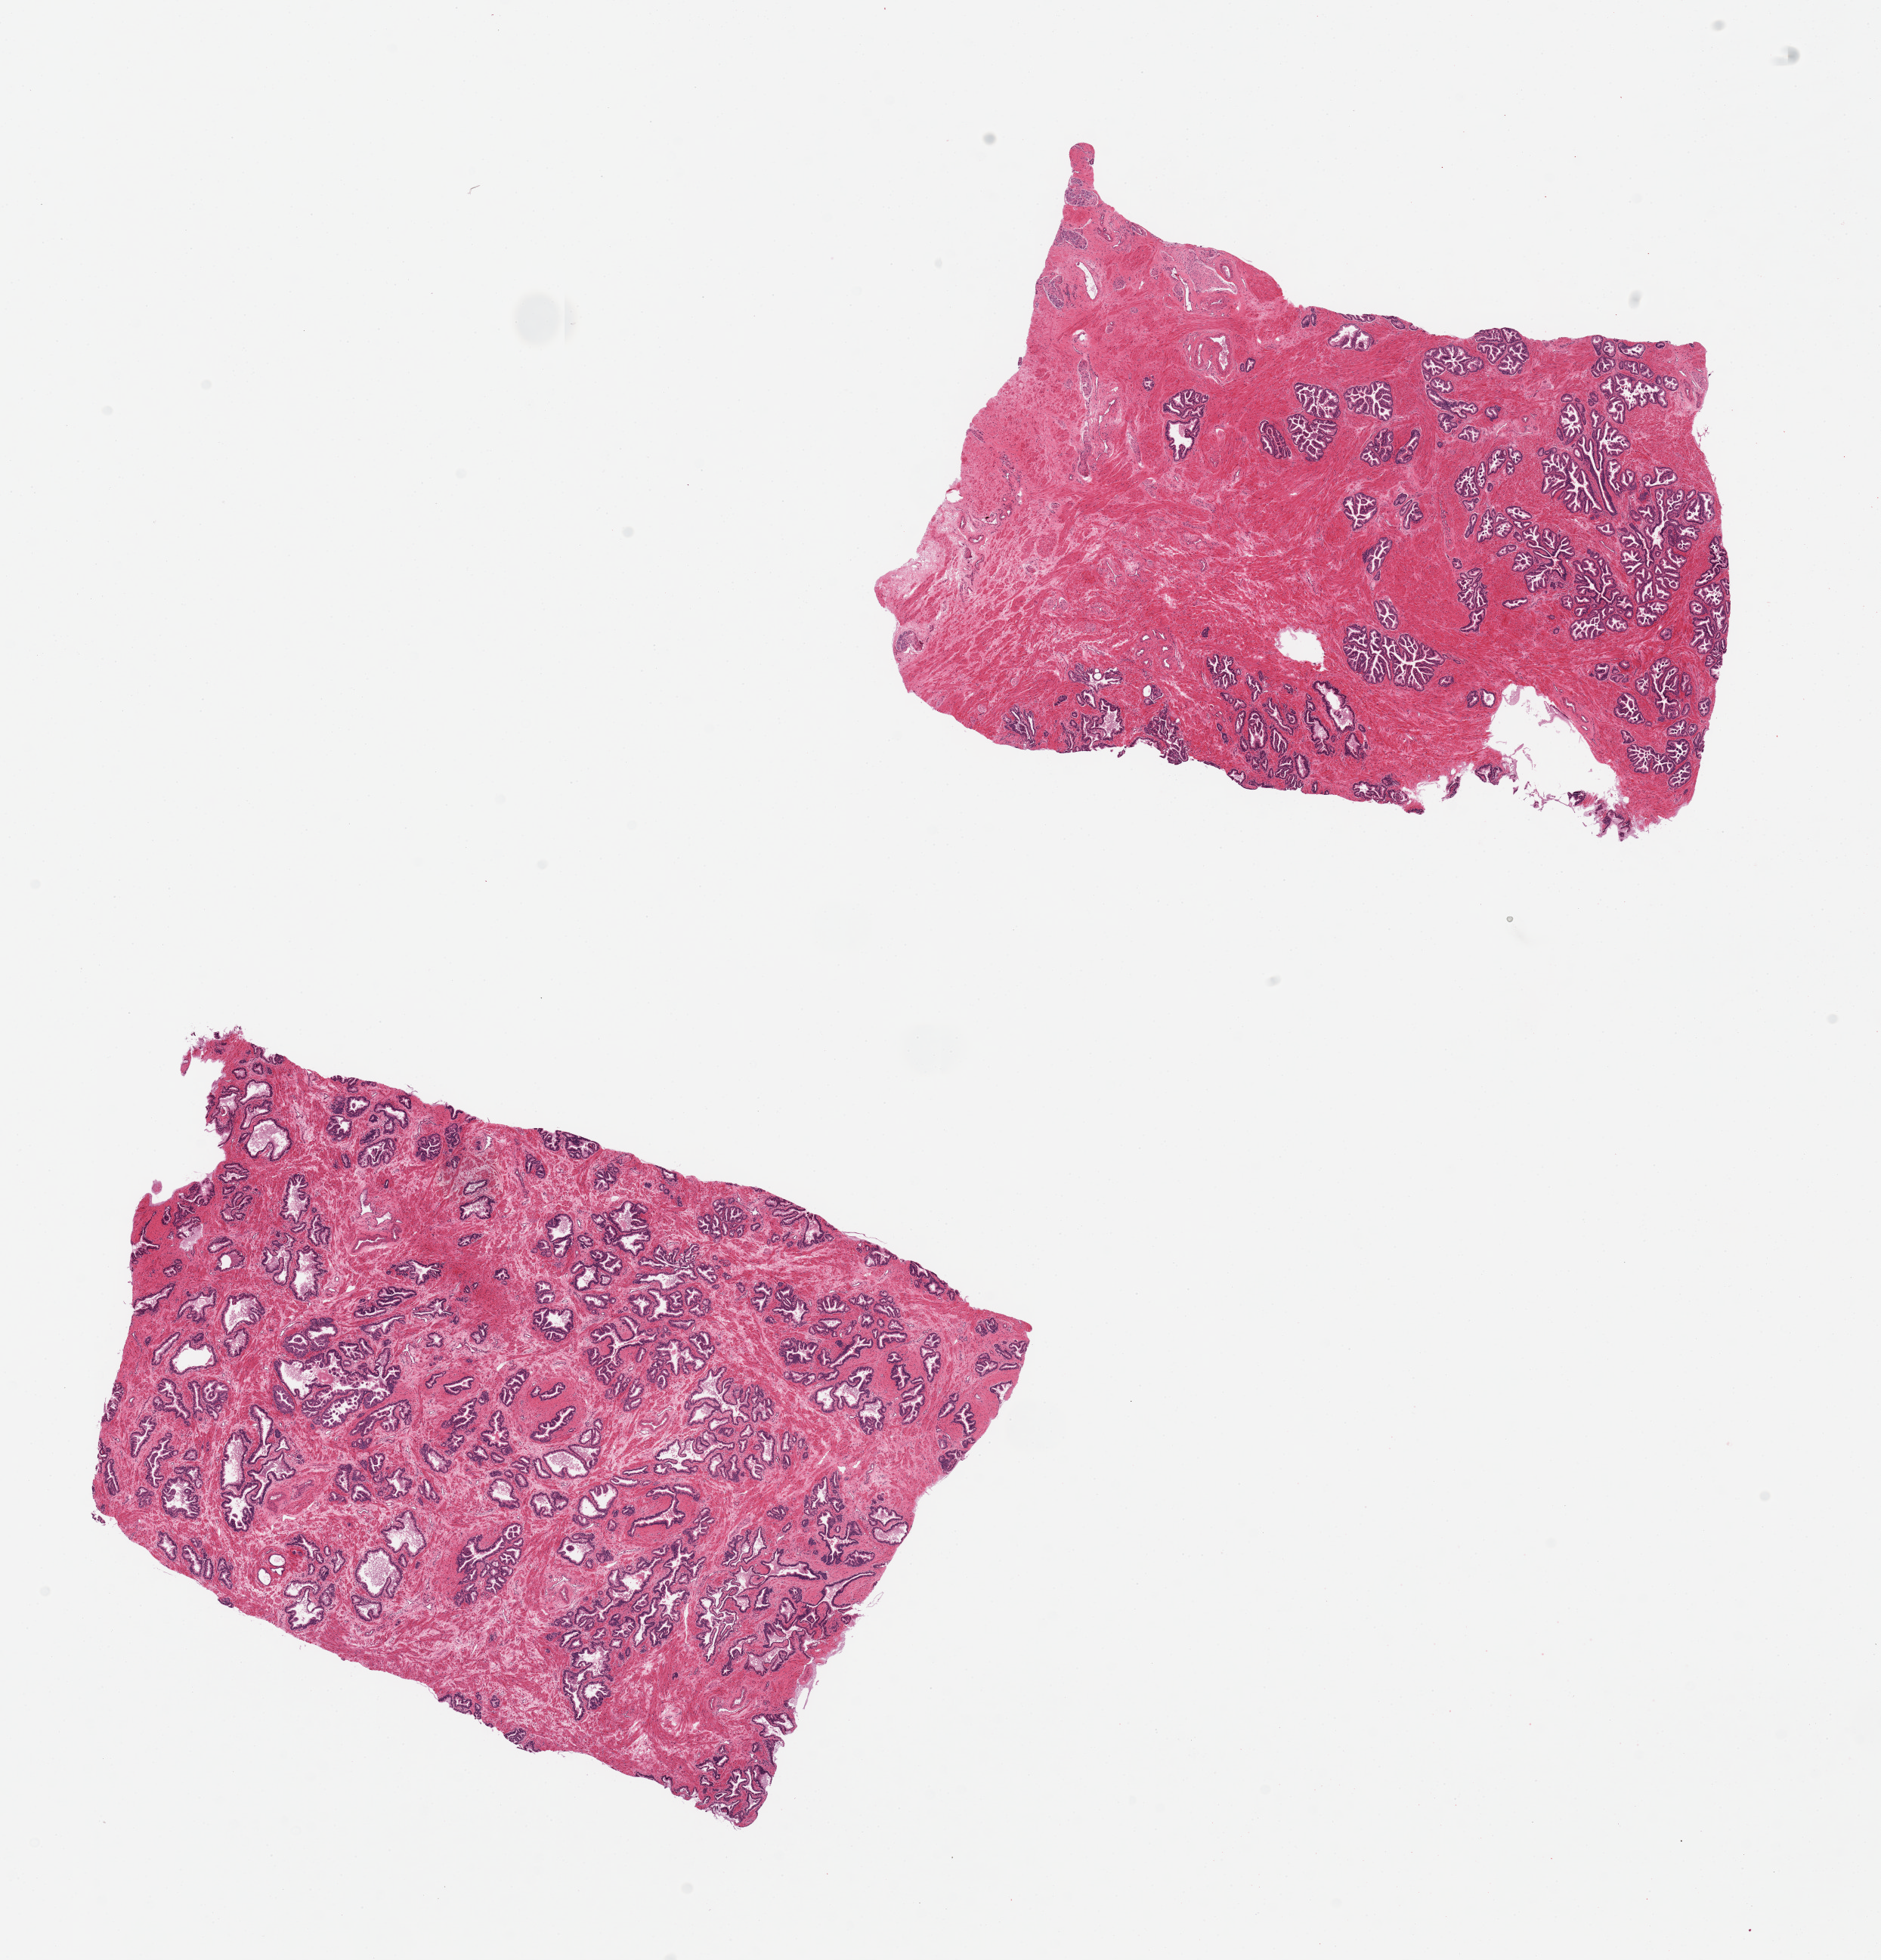
Whole-slide image, hematoxylin and eosin (H&E) stain — low-resolution overview of the scanned area, about 19.7 x 20.5 mm (slide scanned at 20x); PAXgene-fixed, paraffin-embedded tissue; target tissue: prostate; tissue donor sample. Donor: male.
Pathologist's review note for this sample: 2 pieces.